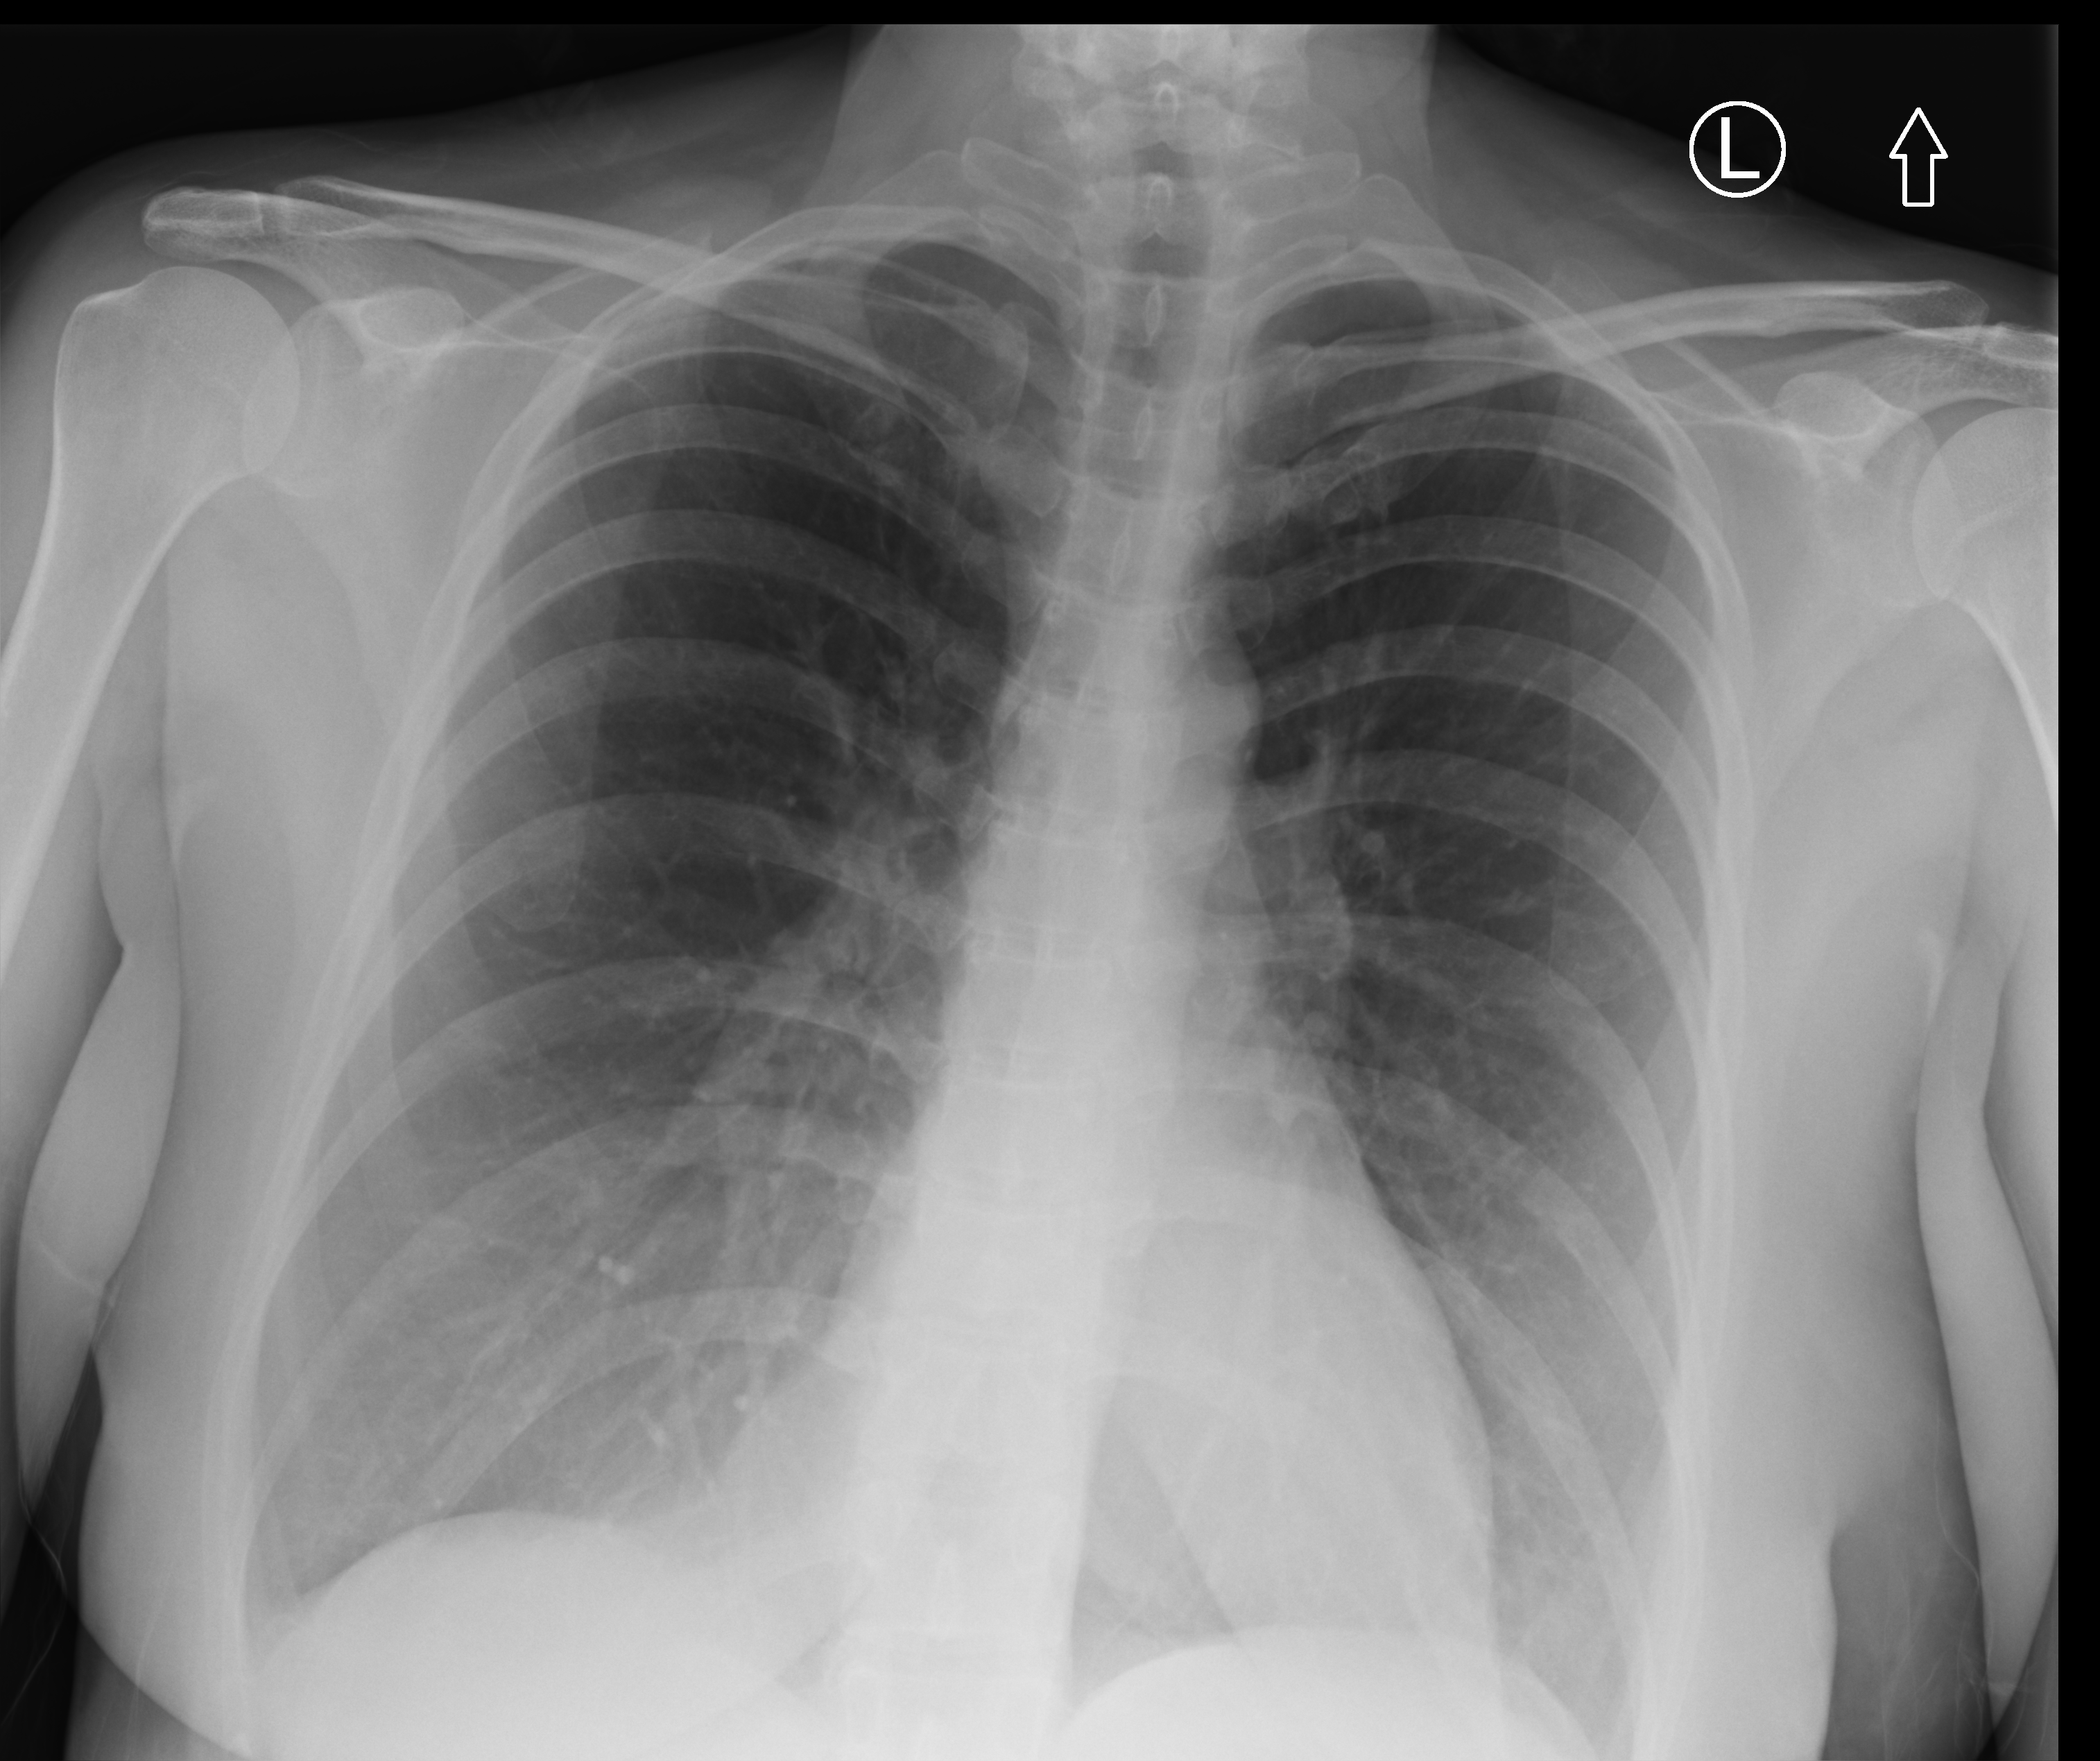
Bedside chest radiograph (computed radiography); anteroposterior (AP) projection. Female patient hospitalised with COVID-19, age 18–59 years.
Admission-level facts for this patient (not findings on this image; timing relative to this image not recorded): admitted to intensive care during this hospital stay: no; mechanically ventilated during this hospital stay: no.